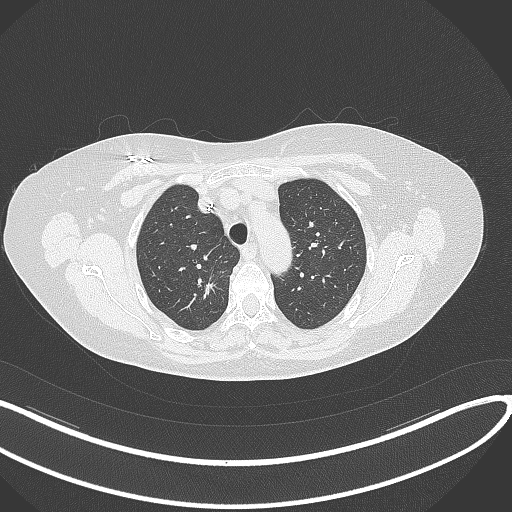
Chest CT, one axial slice; position 258 of 316 along the scan axis; reconstruction kernel B70f; lung window (W 1500 / L -600 HU); 1 mm slice thickness; 512 × 512 image matrix, field of view 400 × 400 mm. Patient: female, 72 years. From the clinical record (not read from this slice): clinical TNM (as recorded): T1c N0 M0.
Structures marked on this image (rectangle marked by the reading radiologist):
- lung tumour (recorded histology: adenocarcinoma): bounding box (x1, y1, x2, y2) in pixels: (194, 275, 222, 304)